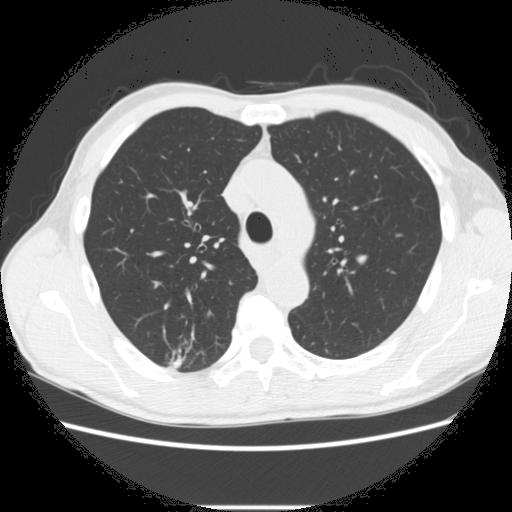
Axial slice from a low-dose chest CT screening exam. Second annual screen. Lung window (W 1500 / L -600 HU). Standard (soft-tissue) reconstruction kernel (STANDARD). Slice 81 of 282 in the series. 512 × 512 image matrix. Male, age 66 years at enrolment.
• Expert-annotated lung lesion, bounding box (x1, y1, x2, y2) in pixels: (163, 340, 221, 379).
• The screening reader recorded 5 non-calcified nodules or masses ≥4 mm on this exam (right lower lobe, right upper lobe, right upper lobe, right upper lobe, left lower lobe); which of them this box marks is not recorded.
• Official screen result: positive, change unspecified: nodule(s) >= 4 mm or enlarging nodule(s), mass(es), or other non-specific abnormalities suspicious for lung cancer.
• Participant outcome: lung cancer diagnosed 75 days after this screen — adenocarcinoma, NOS, right upper lobe, undifferentiated (G4), stage IA (AJCC 6th edition), 20 mm at pathology.